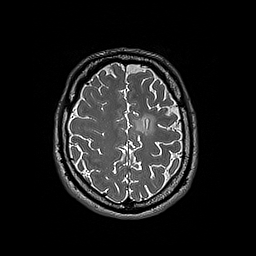
Brain MRI from a brain-tumour surgery series, one axial slice. Position 58 of 192 along the scan axis. 1 mm slice thickness. 256 × 256 image matrix, field of view 250 × 250 mm. Case-level facts recorded for this patient, not image findings: histopathology: Oligodendroglioma; WHO grade: 3; IDH mutation: yes; tumour location: Left Frontal.
Annotated regions visible in this slice (outlined manually by an expert reader):
- tumour: bounding box <135,114,157,136> (left, top, right, bottom; pixels)